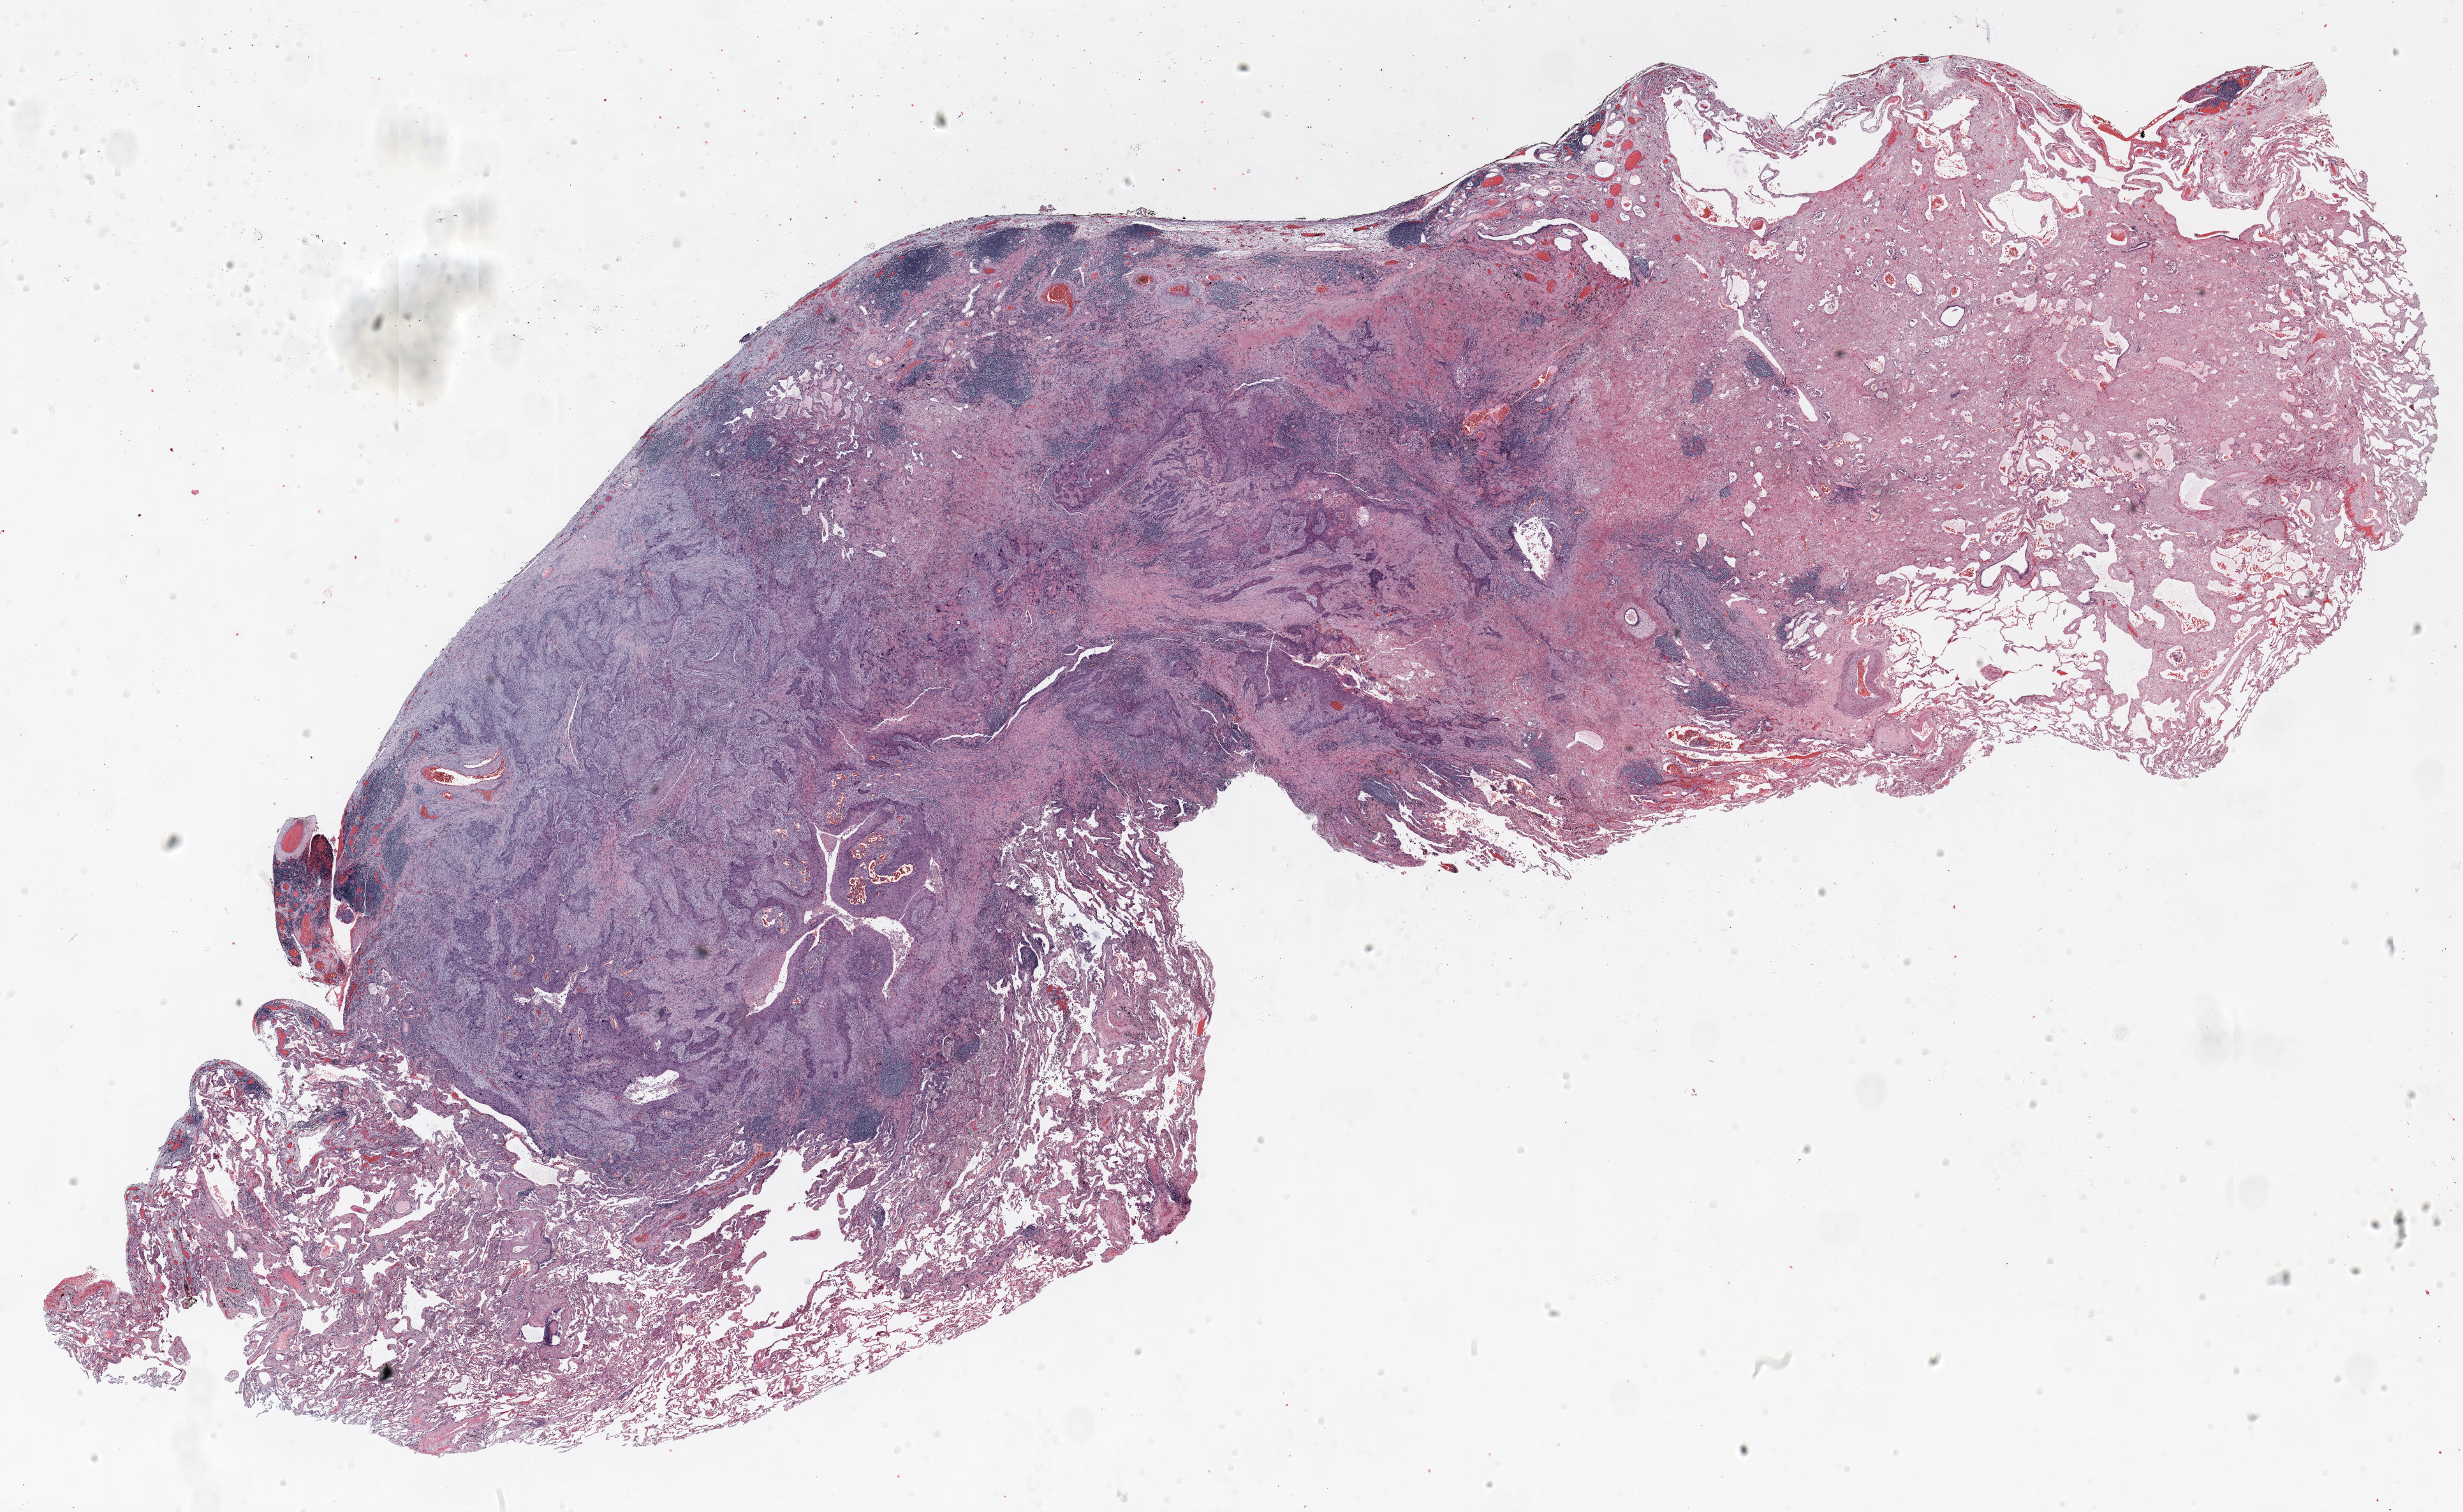
H&E-stained whole-slide image — shown as a low-resolution overview of the whole scanned area (about 31.0 x 19.1 mm); formalin-fixed paraffin-embedded (FFPE) section; lung tissue. Female patient, aged 60 at enrolment. Grade: moderately differentiated (G2).
Tumour size (pathology): 20 mm. Primary tumour location (clinical record): right upper lobe. Stage (AJCC 6th edition): IA. Participant's lung-cancer diagnosis: Squamous cell carcinoma, keratinizing, NOS. Note: participant had 2 primary lung cancers recorded; fields above describe the first.